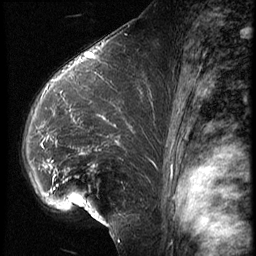
Breast MRI (dynamic contrast-enhanced), one sagittal slice; slice 39 of 62 in the series (ordered by position); 3 images stored at this slice position (order not interpretable as contrast timing); 1.5 T; TE 4.2 ms, TR 9 ms; 2.5 mm slice thickness; 256 × 256 image matrix, field of view 180 × 180 mm. Female patient, age 39 years. From the clinical record (not read from this slice): setting: breast cancer imaged before/during neoadjuvant chemotherapy; receptor status: HER2-positive.
Structures marked on this image (semi-automatic segmentation, software-assisted and operator-edited):
- analysis volume of interest (the breast-tissue region the enhancement analysis was run in; not a lesion): box from (x=21, y=64) to (x=156, y=228) px
- tumour enhancement mask (voxels above the 140 % enhancement threshold inside the analysis volume of interest): (x=43, y=114)–(x=105, y=183)